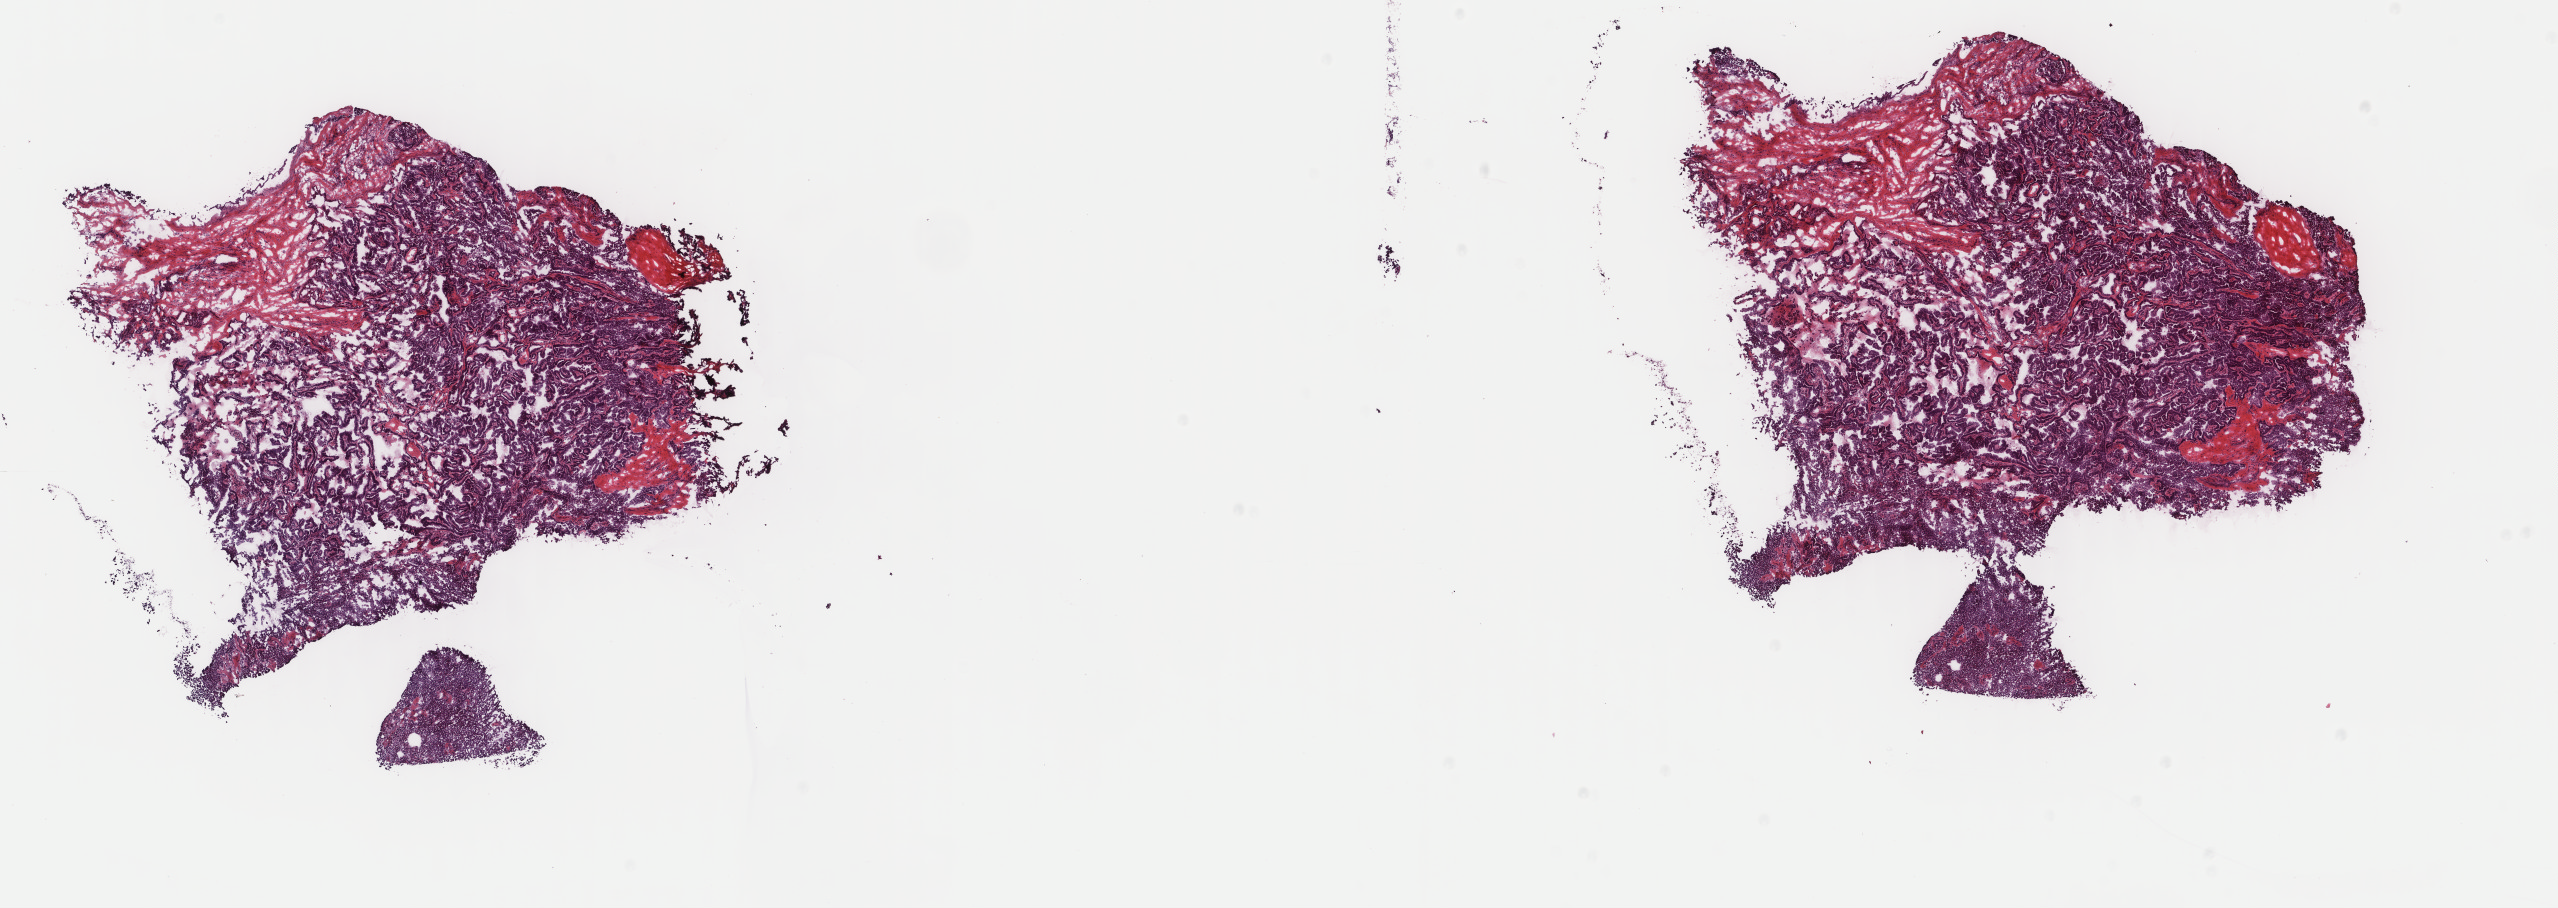
Digitized H&E-stained tissue section (whole slide), shown as a low-resolution overview of the whole scanned area (about 20.3 x 7.2 mm), frozen section from the top of the tissue portion, primary tumour sample from the thyroid. Male patient; age at initial diagnosis 60 years. Slide review estimates, as recorded: tumour cells 70%, tumour nuclei 80%, normal cells 0%, stromal cells 30%, necrosis 0%. Infiltration values recorded for this section: lymphocyte infiltration 2%, monocyte infiltration 0%, neutrophil infiltration 0%.
Laterality: right. AJCC pathologic stage: IVA. Diagnosis: Papillary adenocarcinoma, NOS (thyroid gland). Lymph nodes positive (case pathology): 7 of 27 examined.